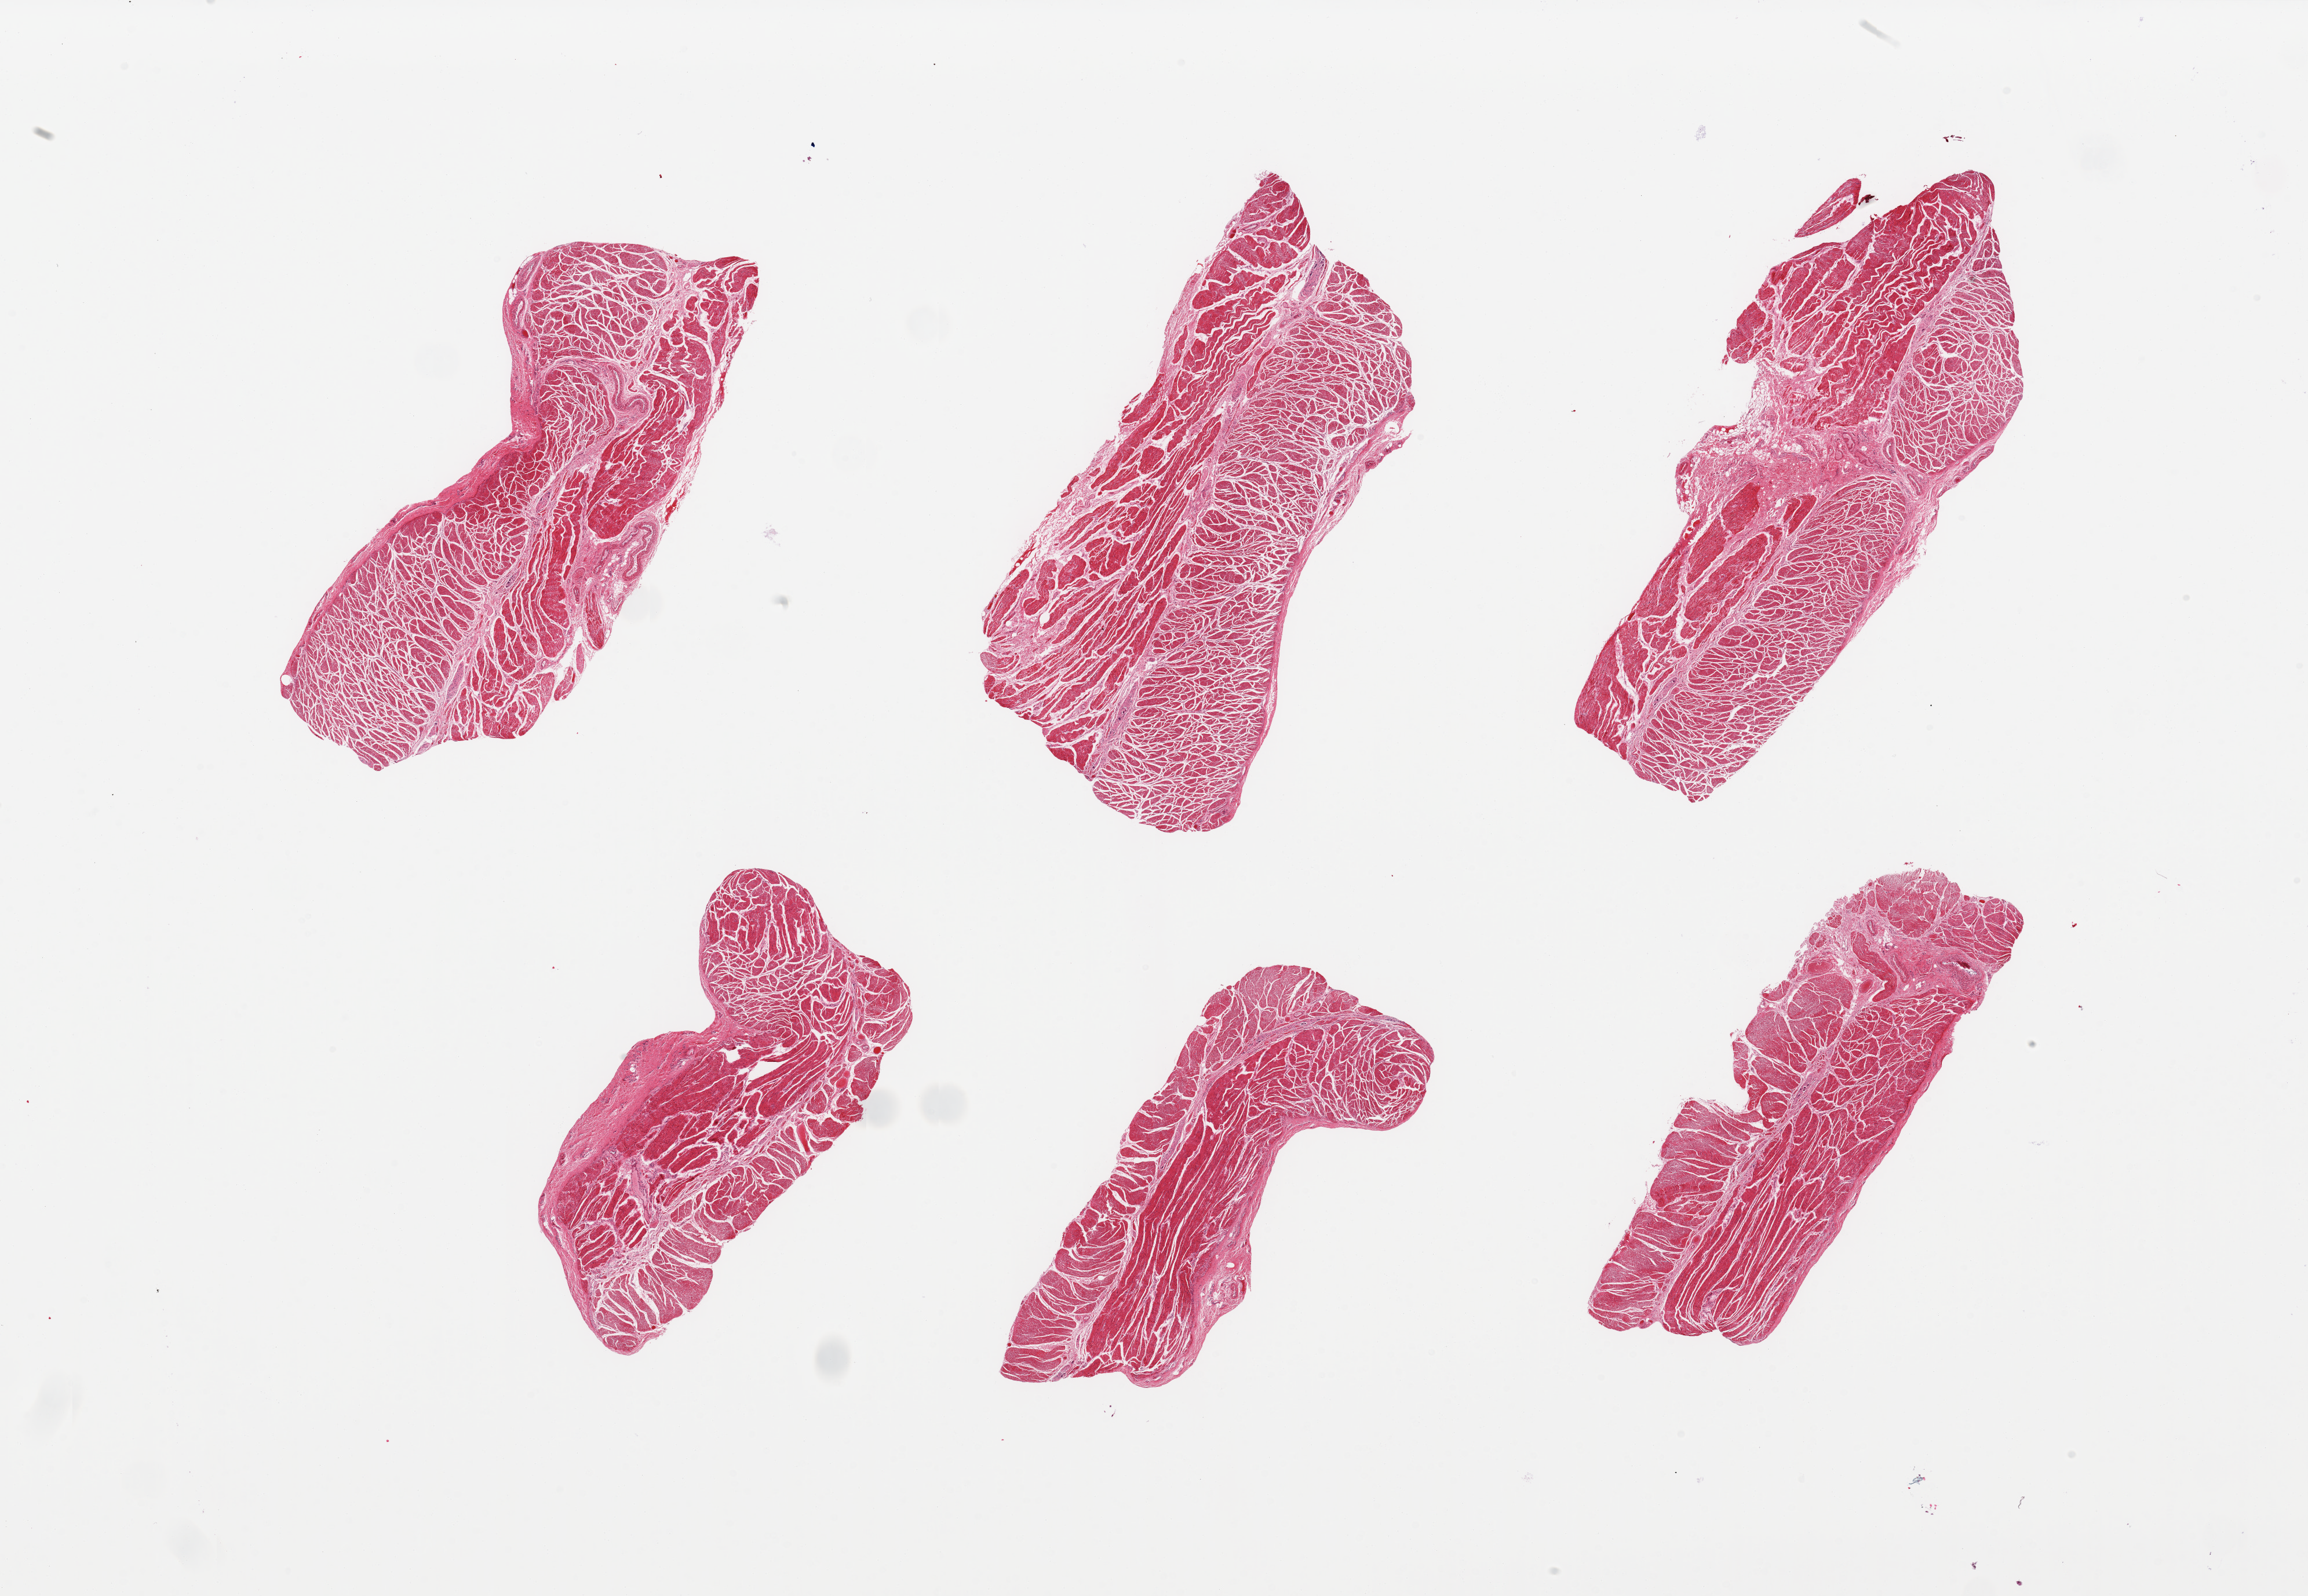
Digitized H&E-stained section, brightfield — a low-resolution overview of the entire scanned area, about 31.5 x 21.8 mm, PAXgene-fixed paraffin-embedded (PFPE) section, section of esophageal muscle (target tissue), tissue donor sample.
Reviewer comment on this tissue sample: 6 pieces, confirmed target muscularis.